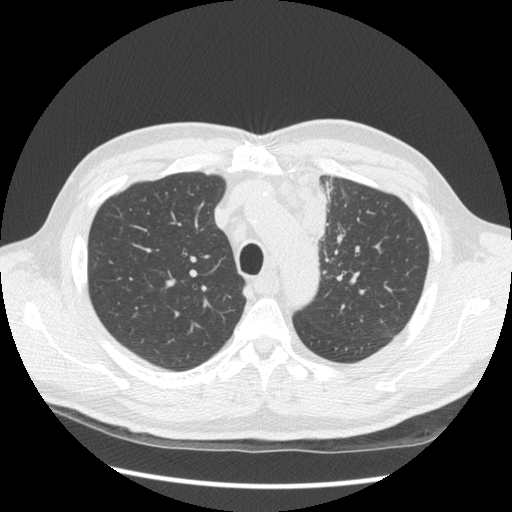
Low-dose screening chest CT, one axial slice; position 106 of 136 along the scan axis; lung window (W 1500 / L -600 HU); 2.5 mm slice thickness; 512 × 512 image matrix, field of view 360 × 360 mm.
Structures marked on this image (outlined manually by an expert reader):
- lesion 1 (tumor, upper lobe of left lung): bounding box [x1, y1, x2, y2] px = [281, 169, 327, 244]